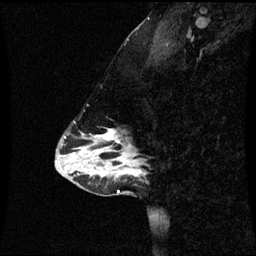
Breast MRI (dynamic contrast-enhanced), one sagittal slice; slice 21 of 60 in the series (ordered by position); dynamic contrast-enhanced series, image 2 of 3 at this slice position (ordered by acquisition); 1.5 T; TE 4.2 ms, TR 8.9 ms; 2 mm slice thickness; 256 × 256 image matrix, field of view 220 × 220 mm. Patient: female, 43 years. Case-level facts recorded for this patient, not image findings: setting: breast cancer imaged before/during neoadjuvant chemotherapy; receptor status: HR-positive, HER2-negative.
Structures marked on this image (semi-automatic segmentation, software-assisted and operator-edited):
- analysis volume of interest (the breast-tissue region the enhancement analysis was run in; not a lesion): box from (x=84, y=134) to (x=144, y=171) px
- tumour enhancement mask (voxels above the 70 % enhancement threshold inside the analysis volume of interest): (x=104, y=134)–(x=124, y=157)